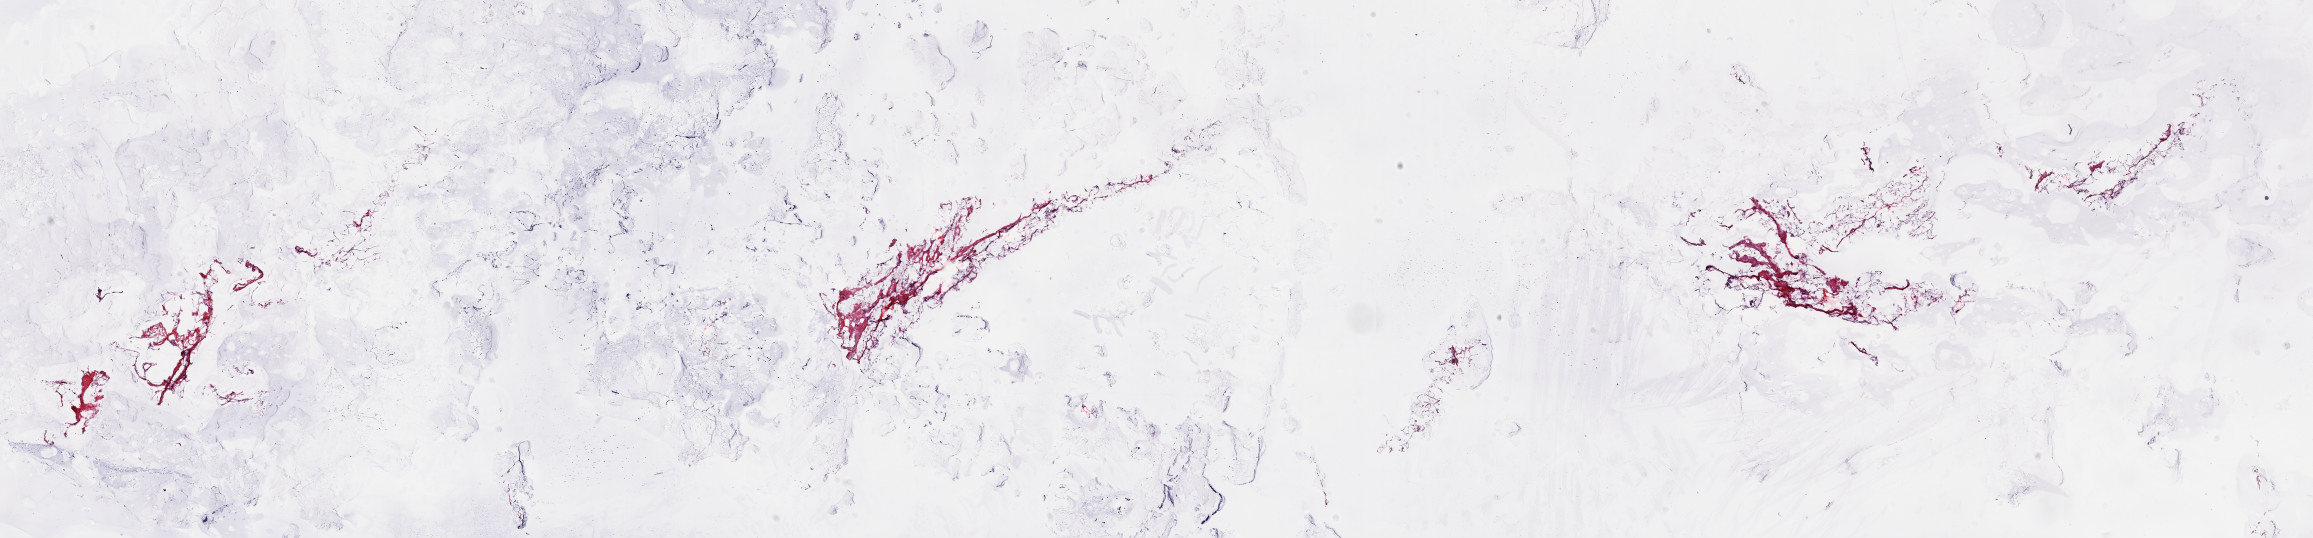
H&E-stained whole-slide image — a low-resolution overview of the entire scanned area, about 36.7 x 8.5 mm (acquisition: 20x scan); frozen section from the top of the tissue portion; breast, solid tissue normal (non-tumour tissue) sample. Patient: female, age at initial diagnosis 84 years. Pathologist review of this section (percent, as recorded): tumour cells 0%, tumour nuclei 0%, normal cells 100%, stromal cells 0%, necrosis 0%. Infiltration values recorded for this section: lymphocyte infiltration 1%, monocyte infiltration 0%, neutrophil infiltration 0%.
* this section: solid tissue normal (non-tumour) sample from the same patient
* patient diagnosis: Infiltrating duct carcinoma, NOS